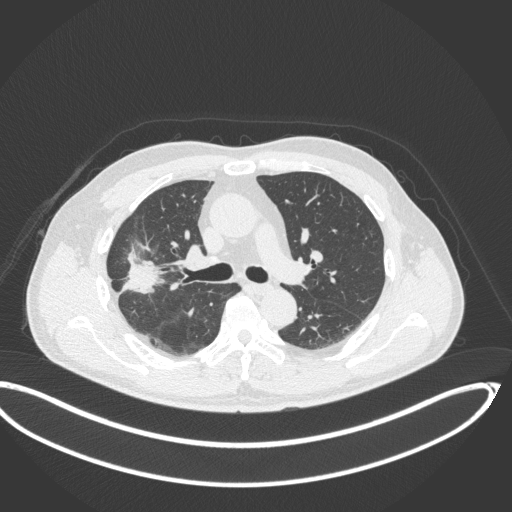
Chest CT, one axial slice. Position 215 of 341 along the scan axis. Reconstruction kernel B31f. 120 kVp. Lung window (W 1500 / L -600 HU). 1 mm slice thickness. 512 × 512 image matrix. Male patient, age 63 years. Case-level facts recorded for this patient, not image findings: clinical TNM (as recorded): T1c N0 M0.
Annotated regions visible in this slice (rectangle marked by the reading radiologist):
- lung tumour (recorded histology: adenocarcinoma): bounding box [x1, y1, x2, y2] px = [117, 250, 162, 300]